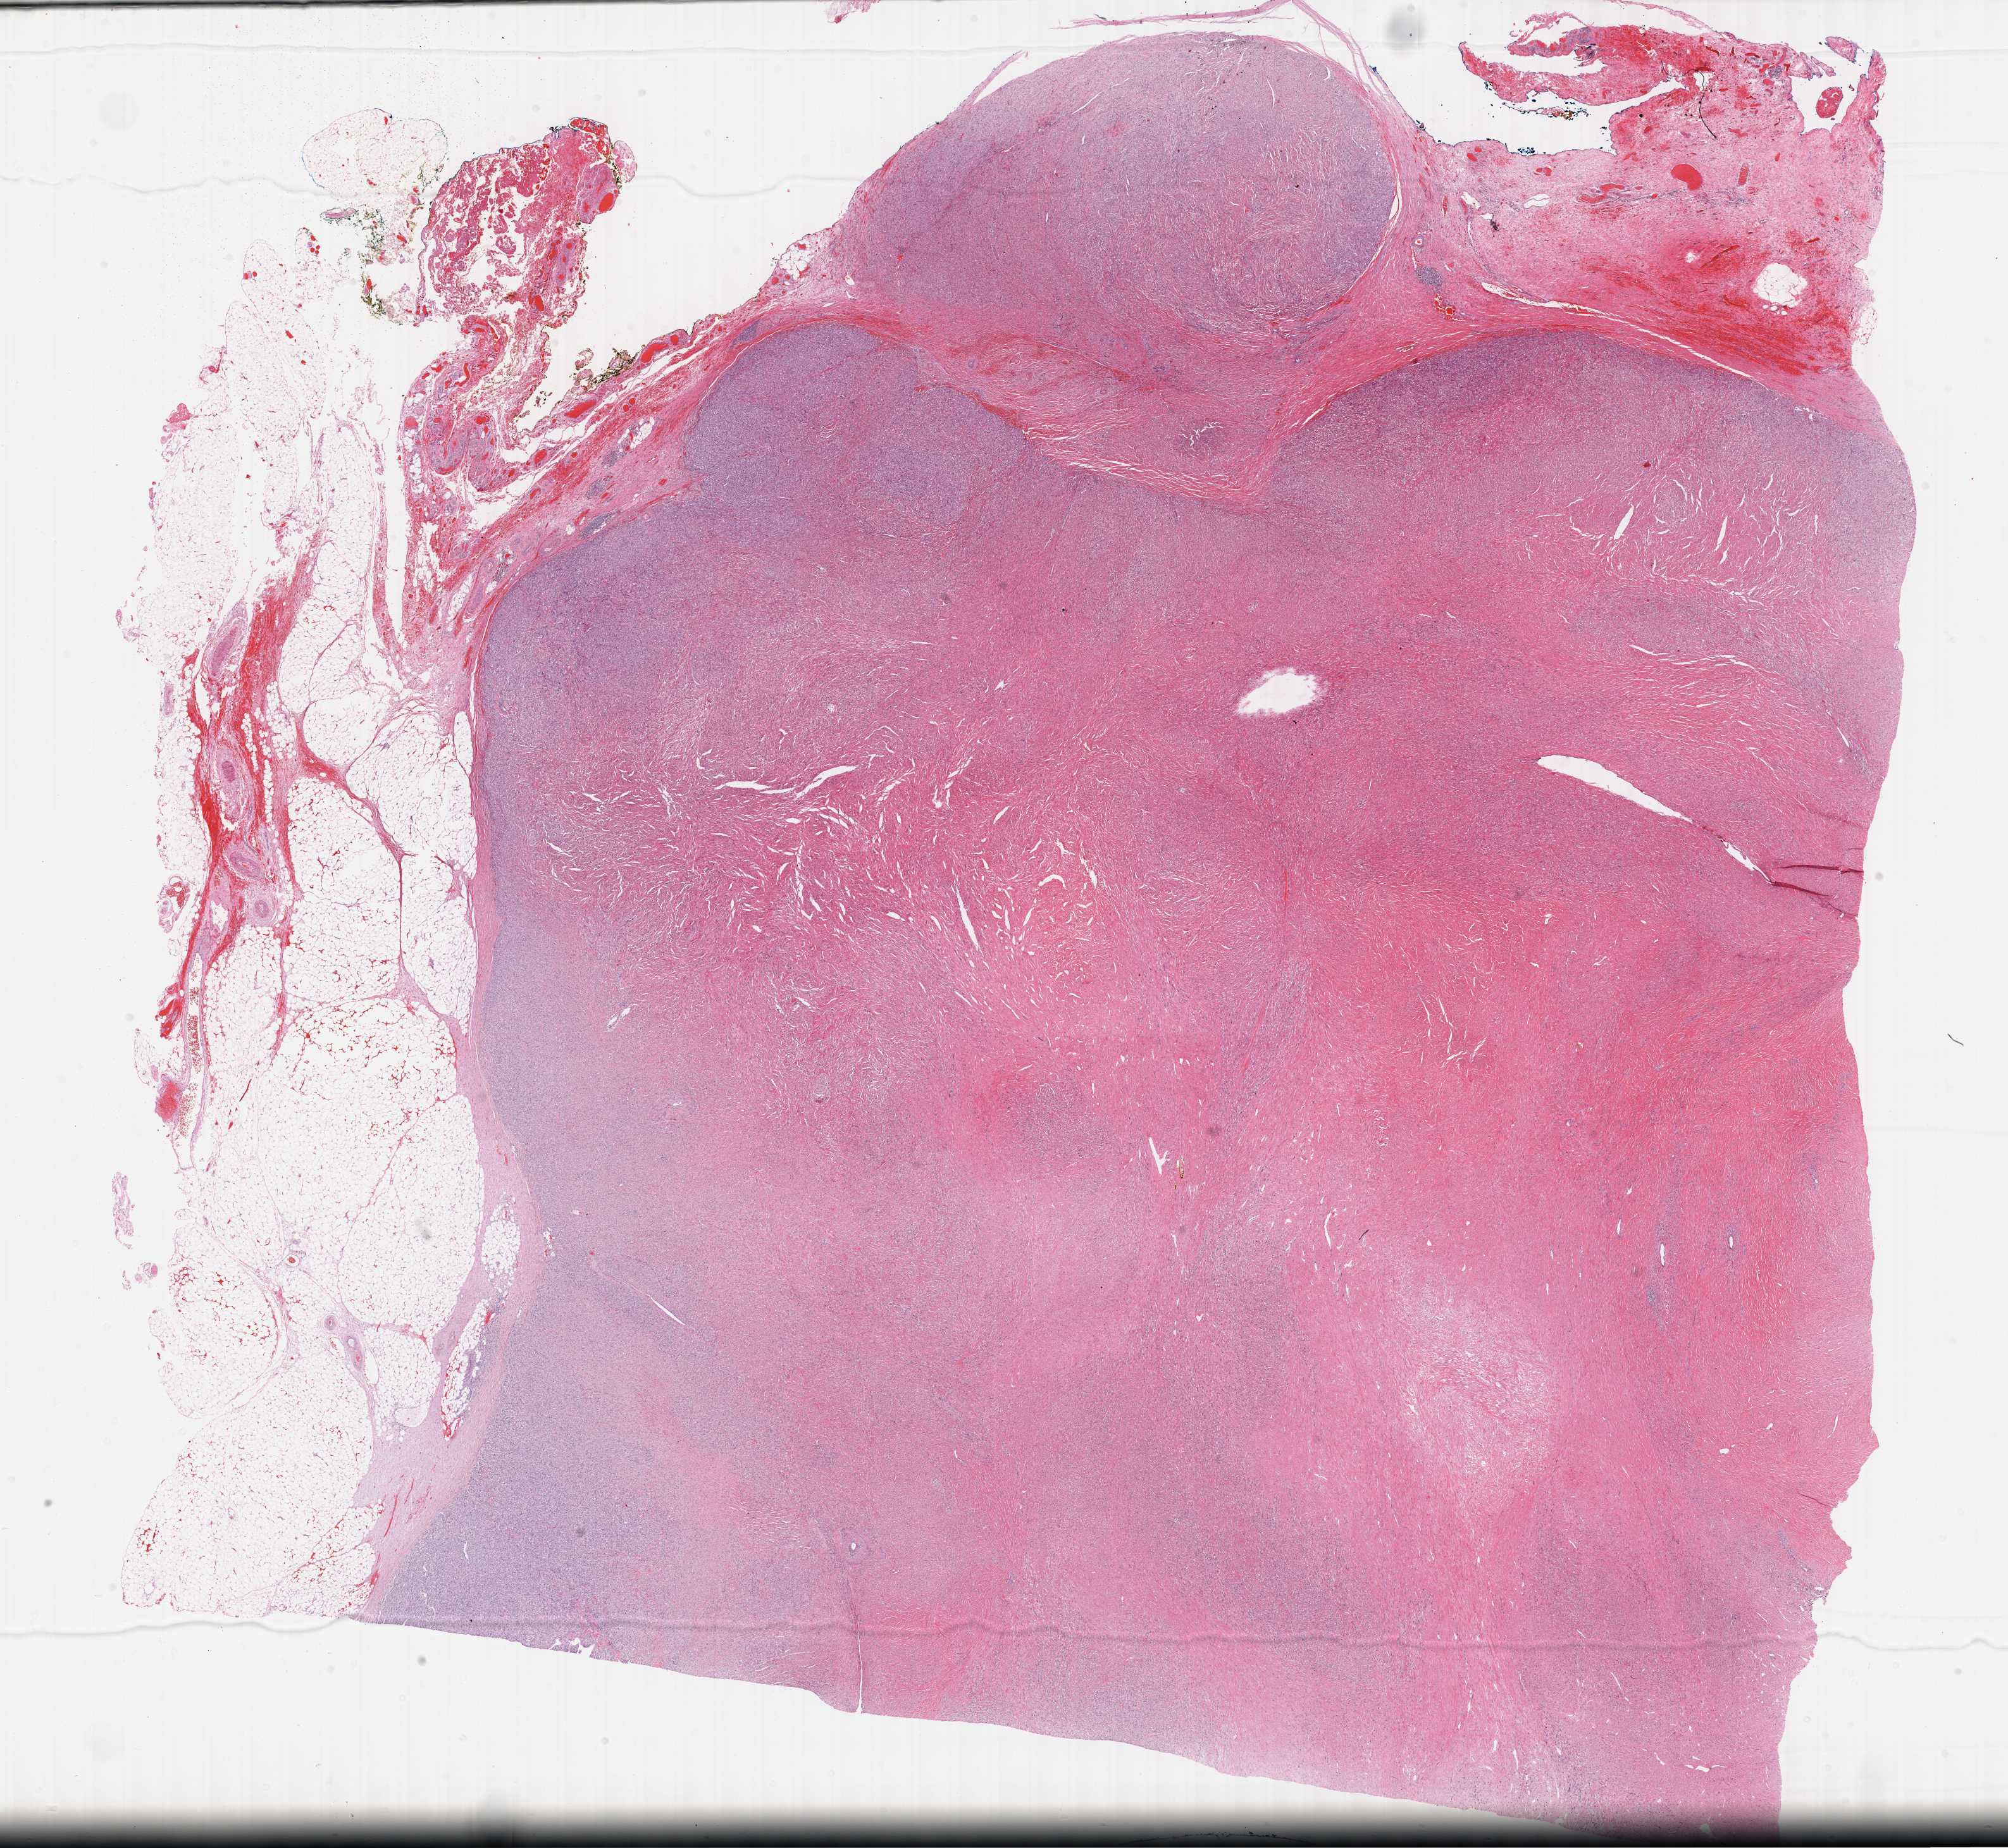
Hematoxylin and eosin (H&E) stained whole-slide image — a low-resolution overview of the entire scanned area, about 25.7 x 23.6 mm (acquisition: 40x scan); FFPE section; primary tumour sample from the retroperitoneum and peritoneum. Patient: female, age at initial diagnosis 66 years.
• diagnosis: Dedifferentiated liposarcoma